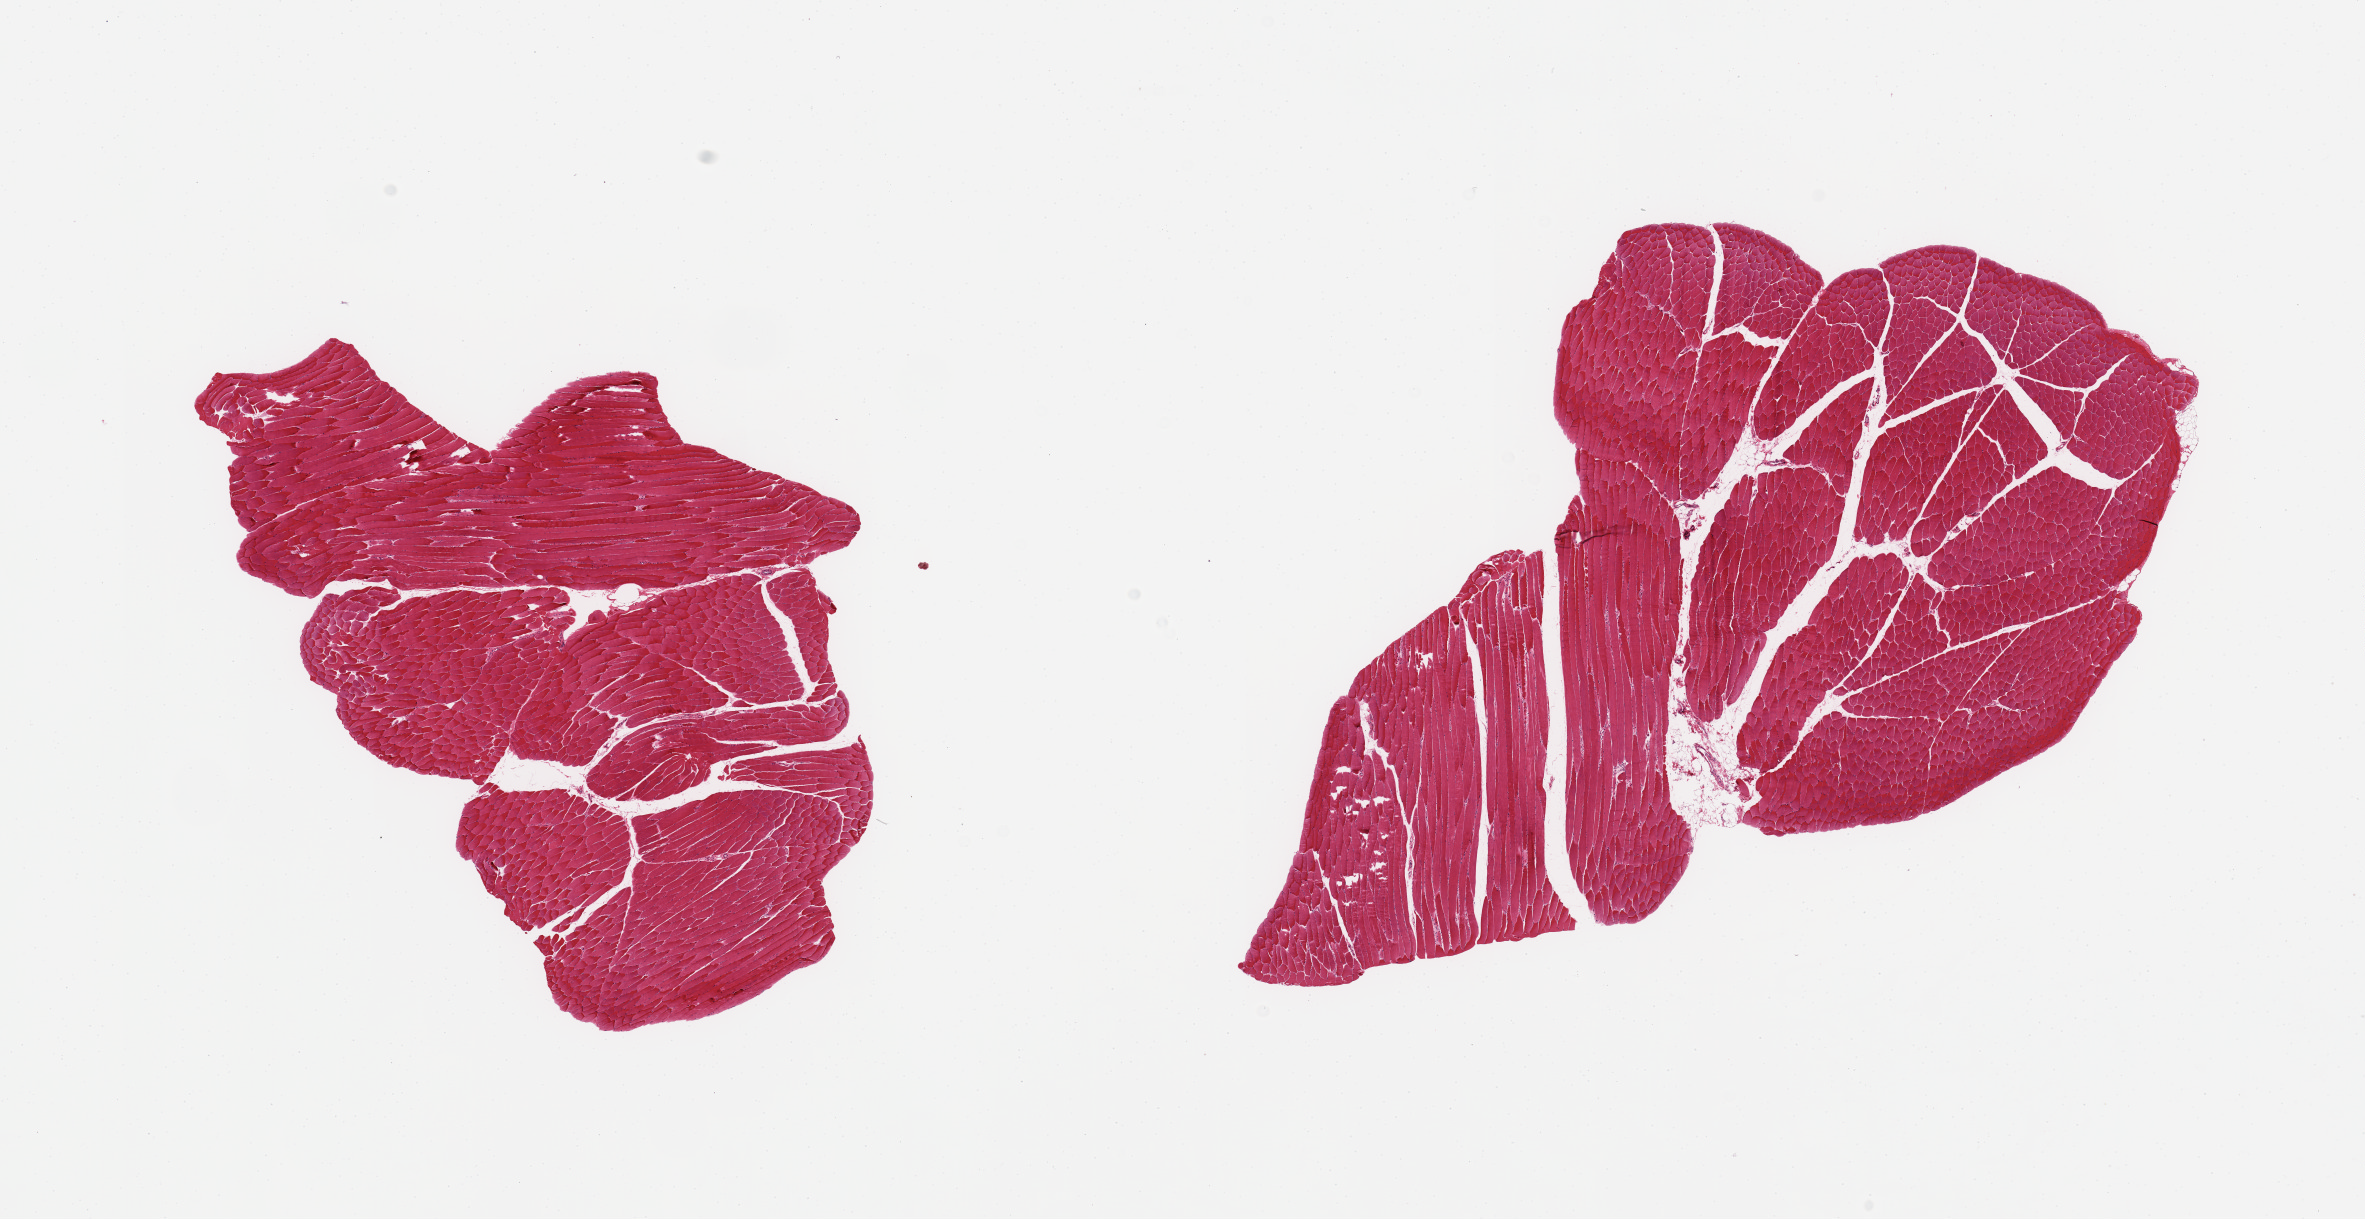
Whole-slide image, hematoxylin and eosin (H&E) stain — a low-resolution overview of the entire scanned area, about 18.7 x 9.6 mm (slide scanned at 20x). PAXgene-fixed, paraffin-embedded tissue. Section of skeletal muscle (target tissue). Donor tissue sample. Female donor.
Pathologist's review note for this sample: 2 pieces; <5% fat content.